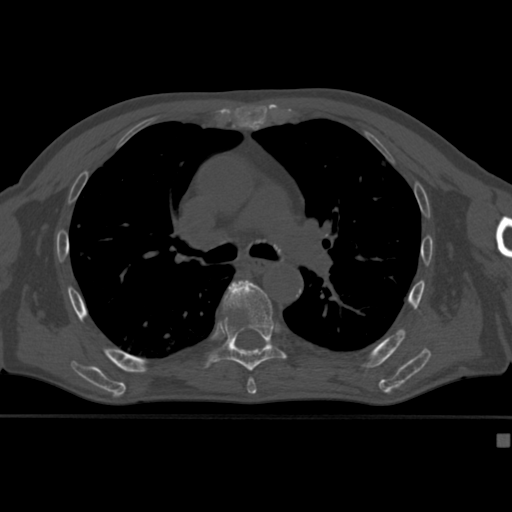
CT including the spine, one axial slice. Position 282 of 430 along the scan axis. 120 kVp. Bone window (W 1800 / L 400 HU). 1.5 mm slice thickness. 512 × 512 image matrix, field of view 337 × 337 mm. Male patient, age 64 years. From the clinical record (not read from this slice): primary cancer: uterus; vertebrae with lytic lesions (as recorded): T1, T4, T5, T7, L5.
Outlined on this slice (semi-automatic segmentation, software-assisted and operator-edited):
- T6 vertebra: bounding box <248,377,254,382> (left, top, right, bottom; pixels)
- T7 vertebra: <204,280,287,374>